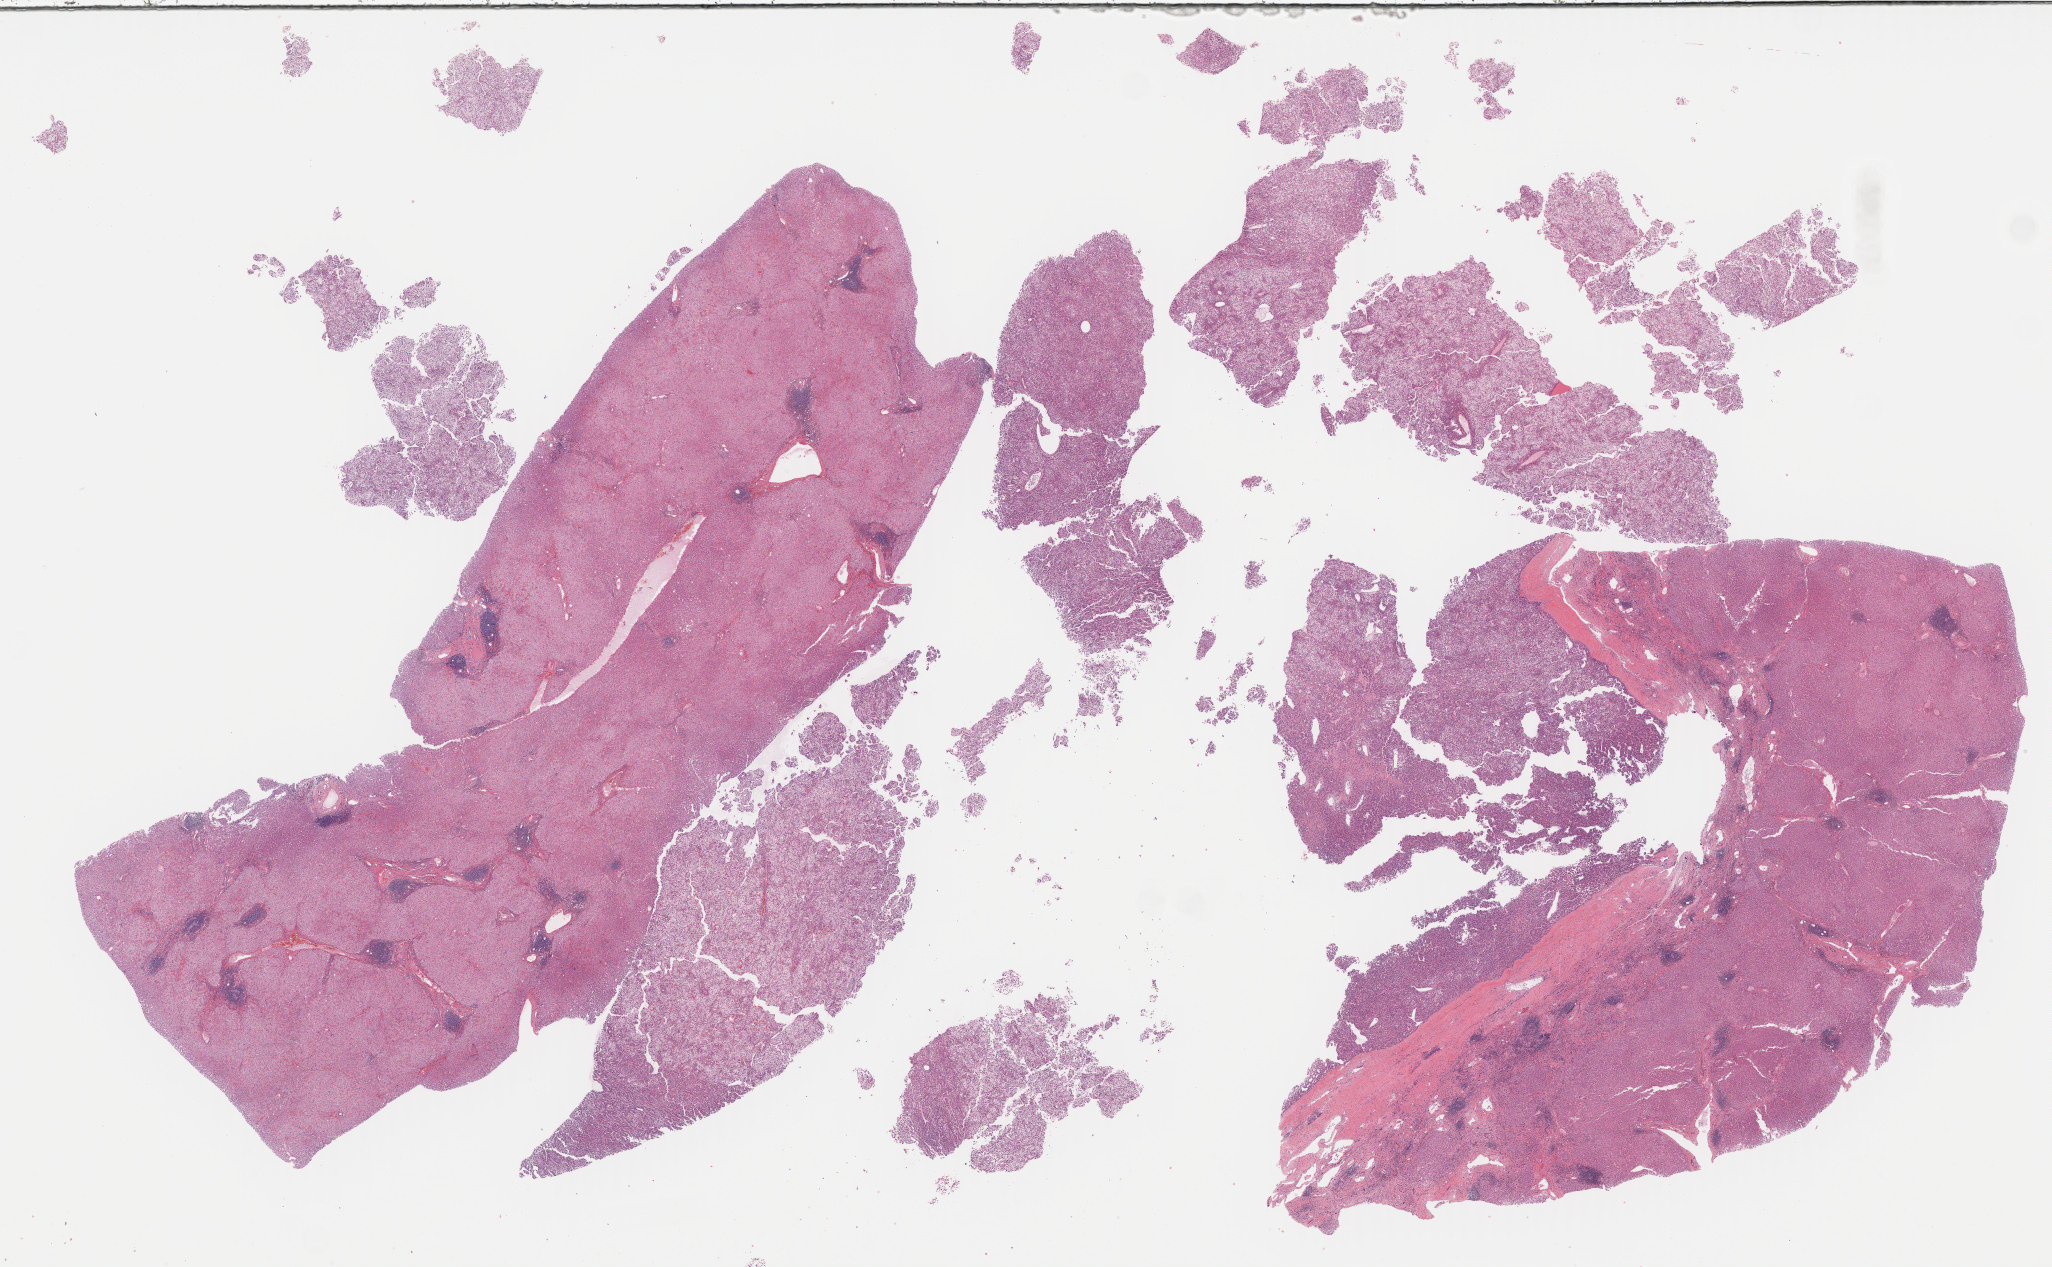
Digitized H&E-stained tissue section (whole slide), low-resolution overview of the scanned area, about 33.2 x 20.5 mm (from a 40x scan). FFPE section. Primary tumour sample from the liver. Female, age 57 years at initial diagnosis. Histologic grade: G2 (moderately differentiated).
AJCC pathologic stage: I. Pathologic diagnosis: Hepatocellular carcinoma, NOS.